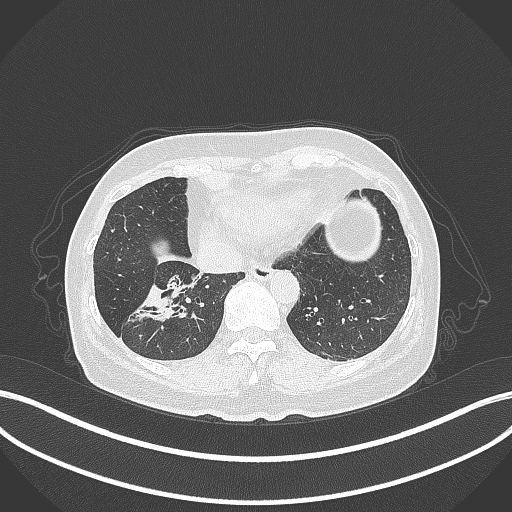
Chest CT, one axial slice. Position 111 of 429 along the scan axis. Reconstruction kernel B70f. Lung window (W 1500 / L -600 HU). 1 mm slice thickness. 512 × 512 image matrix, field of view 400 × 400 mm. Female patient, age 67 years. Case-level facts recorded for this patient, not image findings: clinical TNM (as recorded): T1c N1 M0; histopathological grade: G2-3.
Outlined on this slice (bounding box drawn by a radiologist):
- lung tumour (recorded histology: adenocarcinoma): bounding box <133,278,192,321> (left, top, right, bottom; pixels)